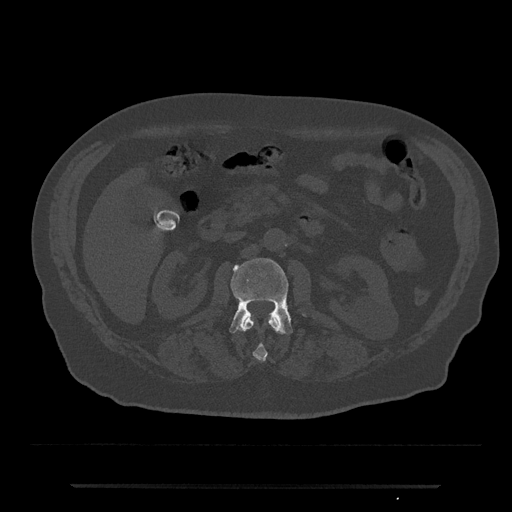
CT including the spine, one axial slice; position 492 of 797 along the scan axis; reconstruction kernel Br40s/3; 120 kVp; bone window (W 1800 / L 400 HU); 0.5 mm slice thickness; 512 × 512 image matrix, field of view 434 × 434 mm. Male patient, age 80 years. From the clinical record (not read from this slice): primary cancer: prostate; vertebrae with lytic lesions (as recorded): L1, T11.
Structures marked on this image (semi-automatically segmented with operator editing):
- L1 vertebra: bounding box [x1, y1, x2, y2] px = [242, 316, 282, 361]
- L2 vertebra: [229, 258, 293, 335]